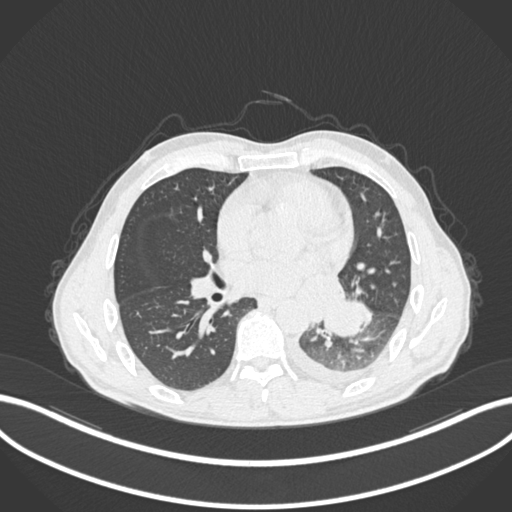
Chest CT, one axial slice; slice 115 of 222 in the series (ordered by position); 120 kVp; lung window (W 1500 / L -600 HU); 1 mm slice thickness; 512 × 512 image matrix. Patient: male, 47 years. From the clinical record (not read from this slice): clinical TNM (as recorded): T3 N1 M1c; histopathological grade: G3.
Structures marked on this image (rectangle marked by the reading radiologist):
- lung tumour (recorded histology: small cell carcinoma): bounding box [x1, y1, x2, y2] px = [318, 294, 365, 339]